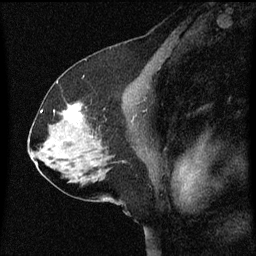
Breast MRI (dynamic contrast-enhanced), one sagittal slice; position 35 of 60 along the scan axis; dynamic contrast-enhanced series, image 2 of 3 at this slice position (ordered by acquisition); 1.5 T; TE 4.2 ms, TR 8 ms; 2 mm slice thickness; 256 × 256 image matrix. Patient: female, 58 years.
Outlined on this slice (semi-automatically segmented with operator editing):
- analysis volume of interest (the breast-tissue region the enhancement analysis was run in; not a lesion): box from (x=56, y=104) to (x=95, y=137) px
- tumour enhancement mask (voxels above the 70 % enhancement threshold inside the analysis volume of interest): (x=64, y=106)–(x=83, y=123)